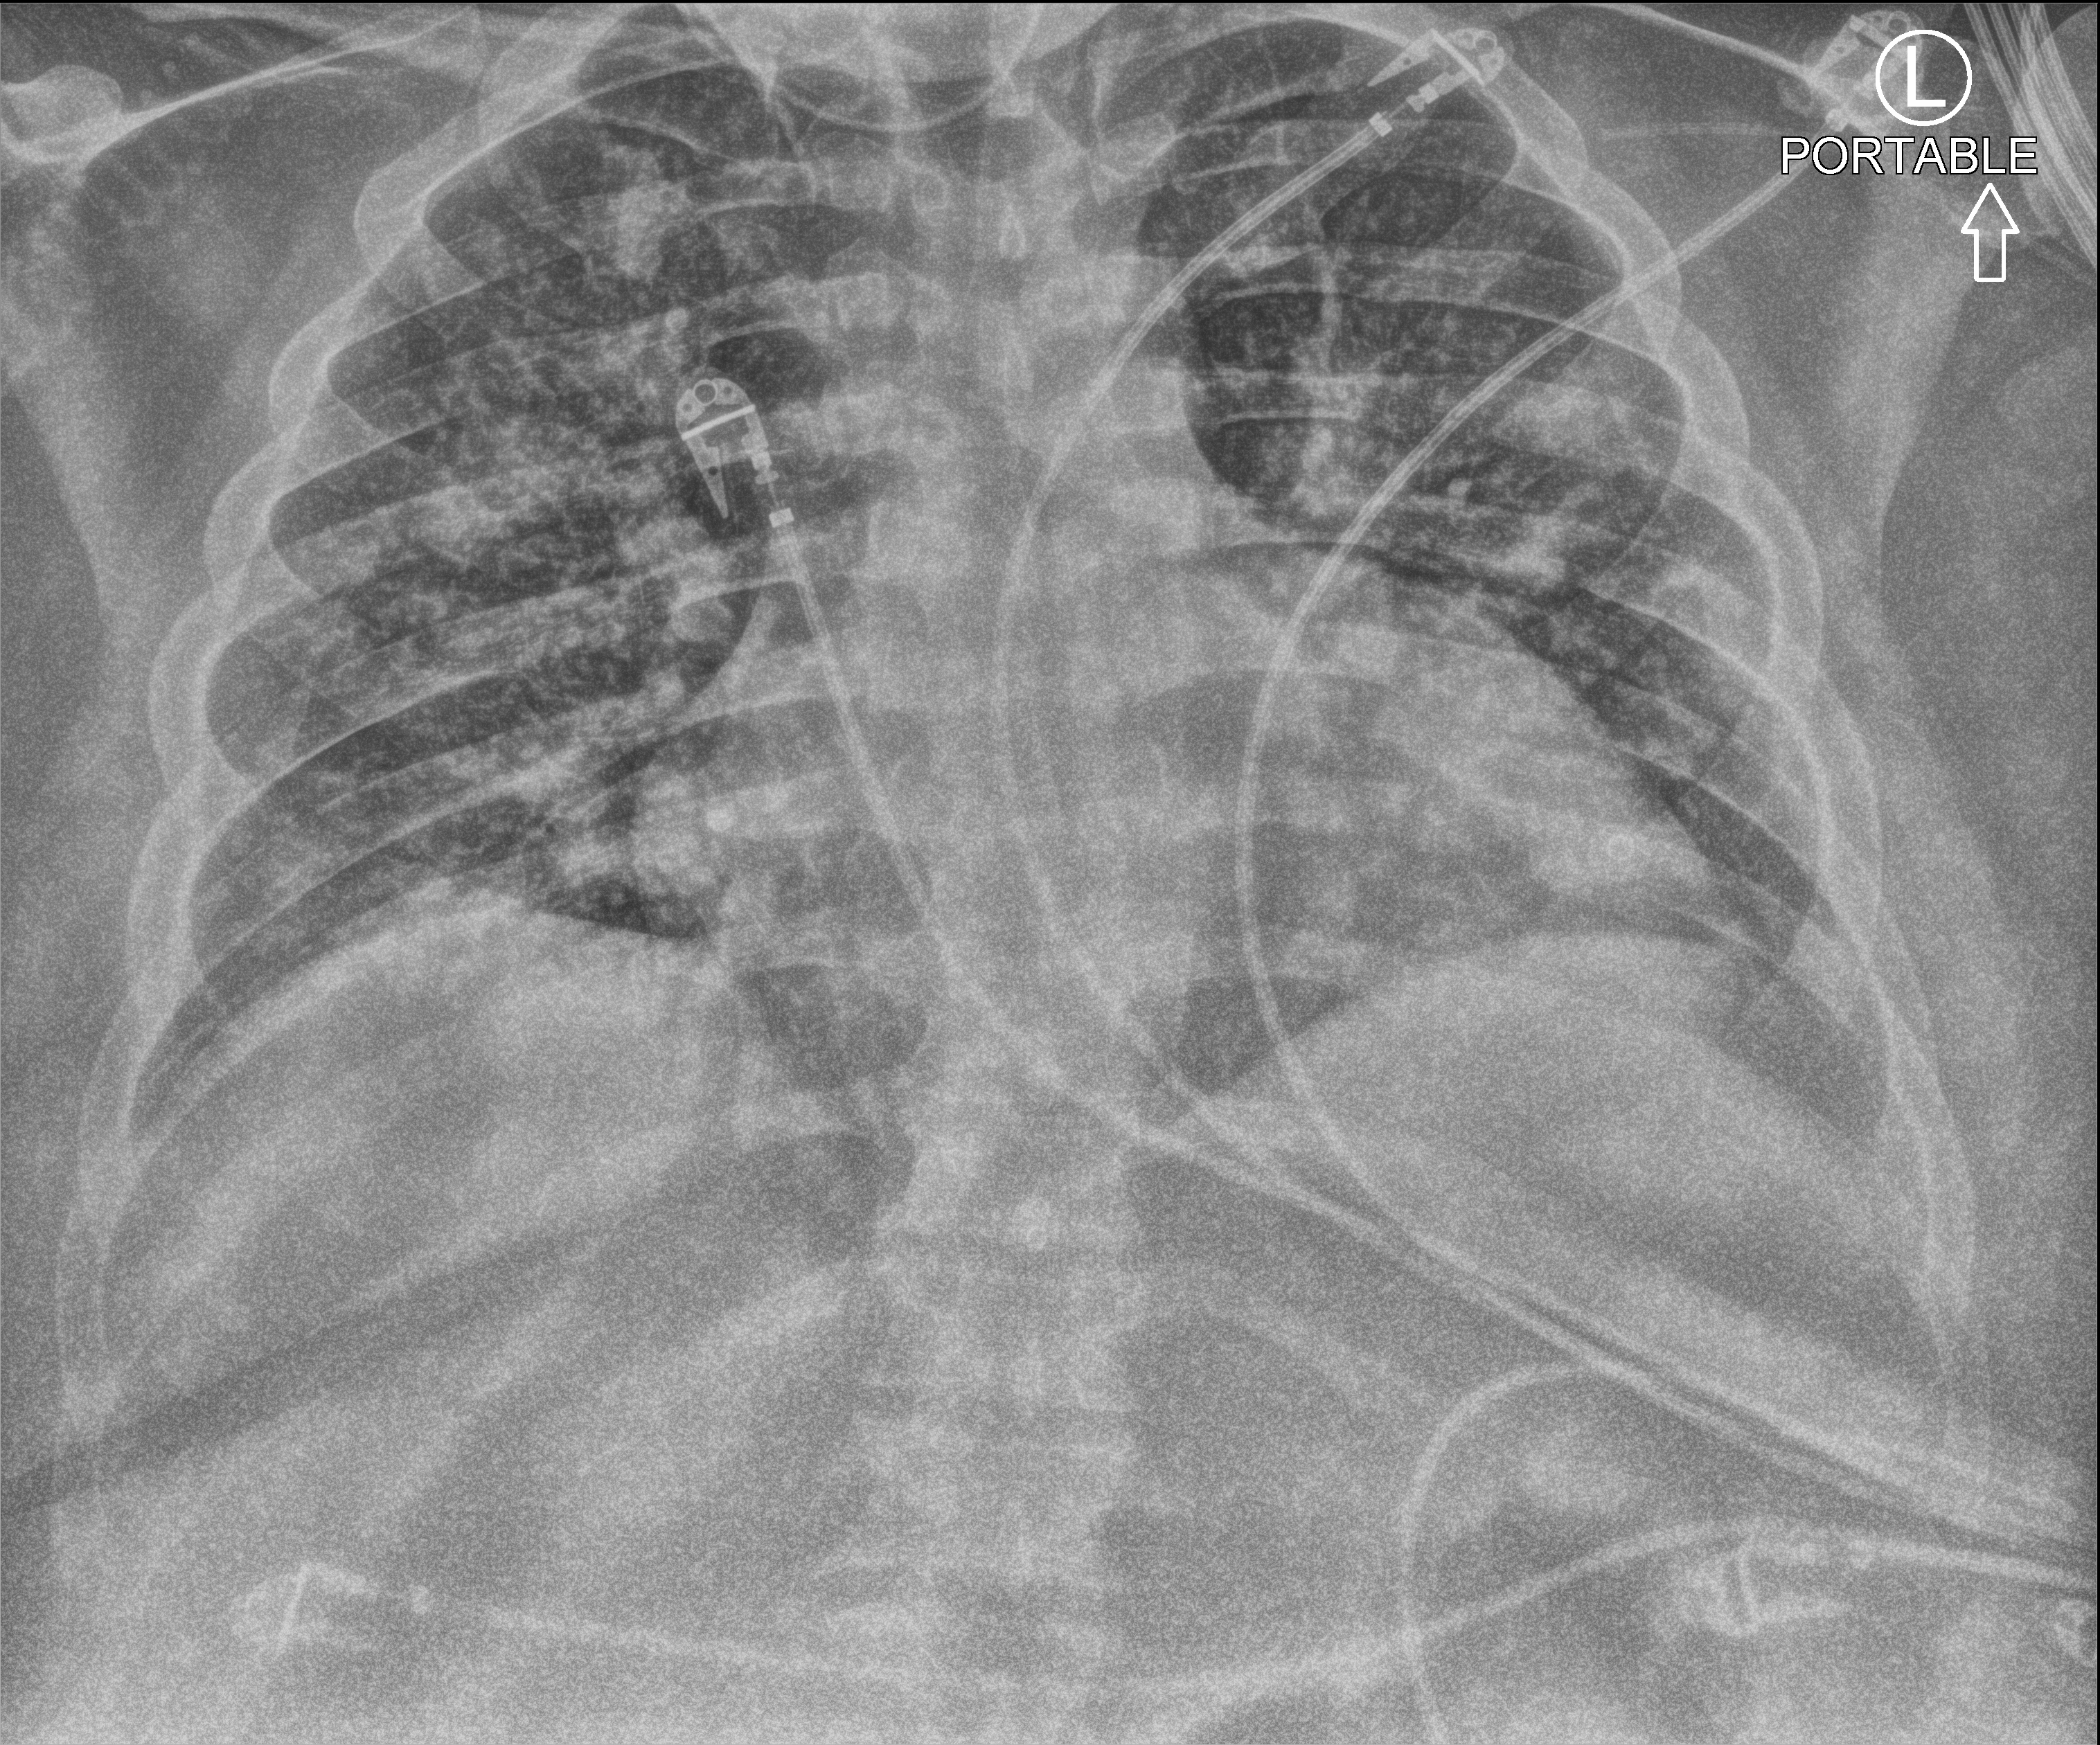
Portable chest radiograph, anteroposterior (AP) projection. Male patient hospitalised with COVID-19, age 18–59 years.
From the hospital-stay record, not from the radiograph (when in the stay this image was taken is not recorded): admitted to intensive care during this hospital stay: yes; length of hospital stay: 19 days.